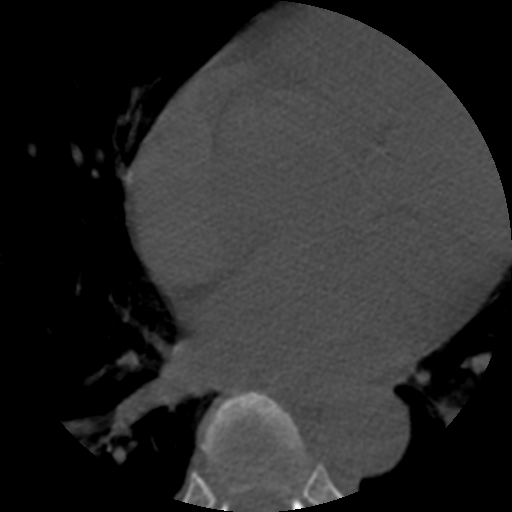
CT including the spine, one axial slice; slice 343 of 508 in the series (ordered by position); reconstruction kernel STANDARD; 120 kVp; bone window (W 1800 / L 400 HU); 1.25 mm slice thickness; 512 × 512 image matrix, field of view 160 × 160 mm. Patient age 57 years. From the clinical record (not read from this slice): primary cancer: prostate.
Structures marked on this image (semi-automatically segmented with operator editing):
- T6 vertebra: bounding box <203,391,307,493> (left, top, right, bottom; pixels)
- T7 vertebra: <220,461,308,512>